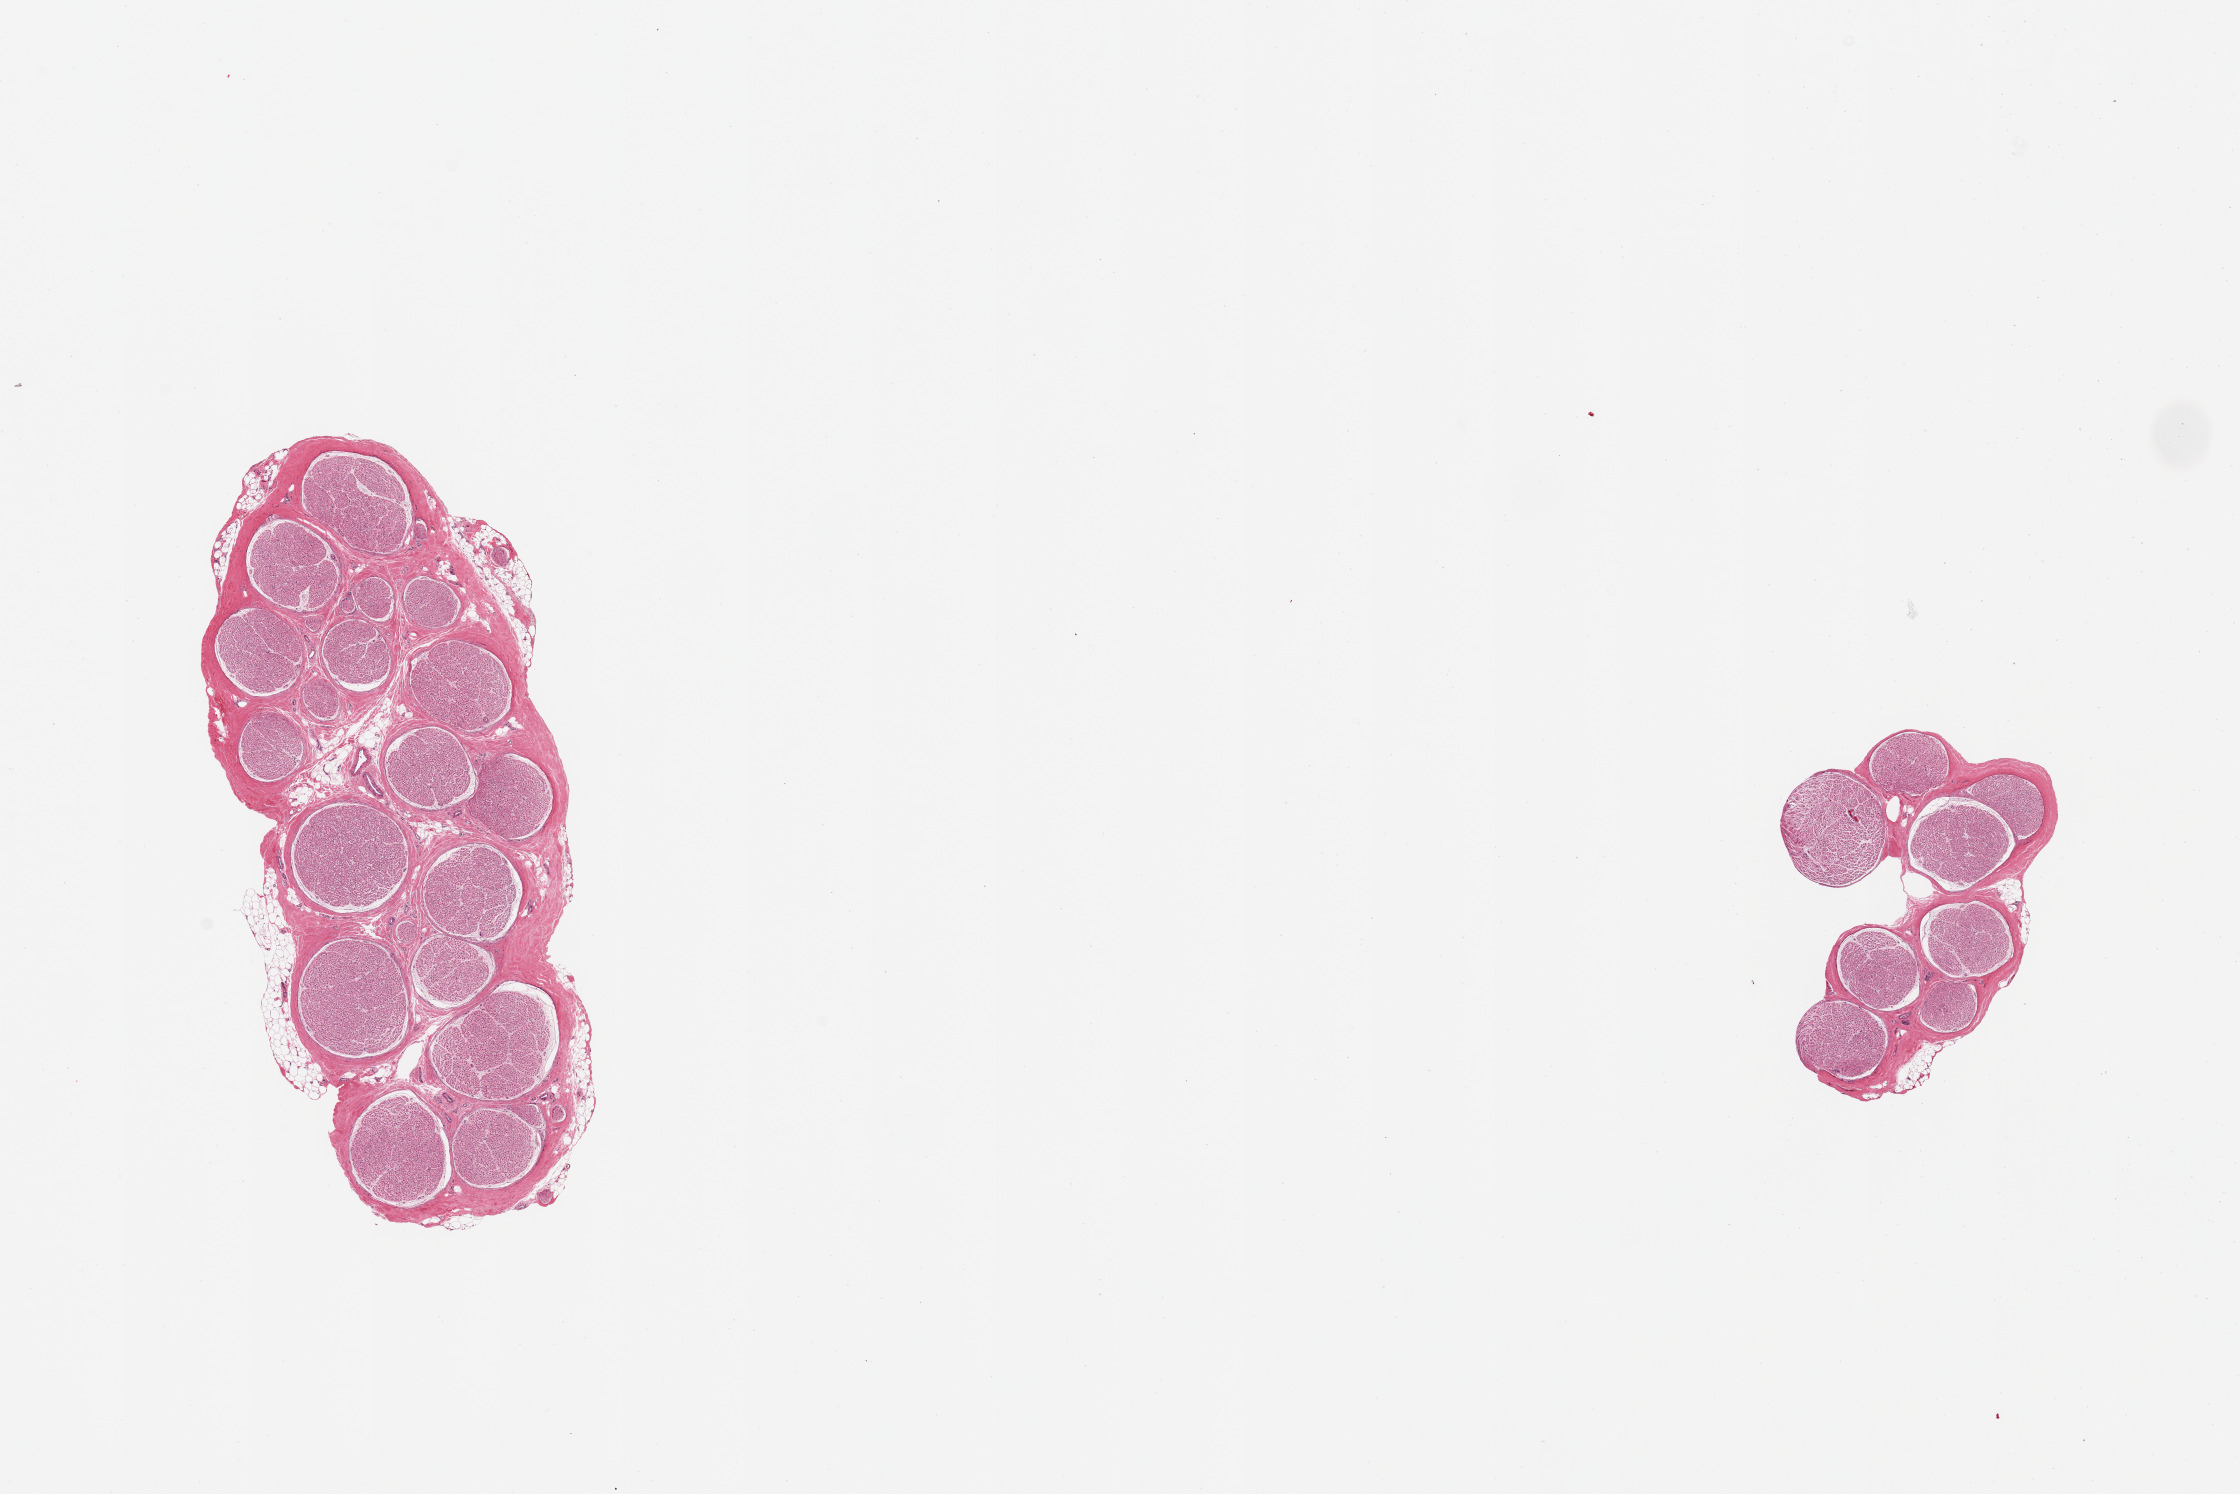
Digitized haematoxylin and eosin-stained section, shown as a low-resolution overview of the whole scanned area (about 17.7 x 11.8 mm), PAXgene-fixed paraffin-embedded (PFPE) section, sampled site (target tissue): tibial nerve, tissue donor sample. Donor sex: male.
* review note (as recorded): 2 pieces; well trimmed; <5% internal fat